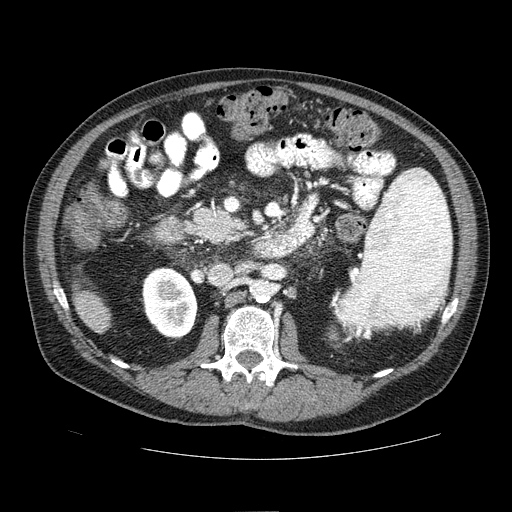
Contrast-enhanced abdominal CT (liver protocol), one axial slice; slice 19 of 81 in the series (ordered by position); one of 2 acquisitions stored at this slice position; soft-tissue window (W 400 / L 40 HU); 512 × 512 image matrix. Case-level facts recorded for this patient, not image findings: diagnosis: hepatocellular carcinoma (patient treated with transarterial chemoembolisation; whether this scan precedes or follows treatment is not stated here); TNM stage (as recorded): Stage-IIIA; Child-Pugh class: A; tumour differentiation: well differentiated; tumour nodularity: multinodular.
Annotated regions visible in this slice (semi-automatic segmentation, software-assisted and operator-edited):
- liver parenchyma outside the tumour (the mass and vessels are separate outlines, so this box may not span the whole liver): bounding box (x1, y1, x2, y2) in pixels: (72, 283, 110, 332)